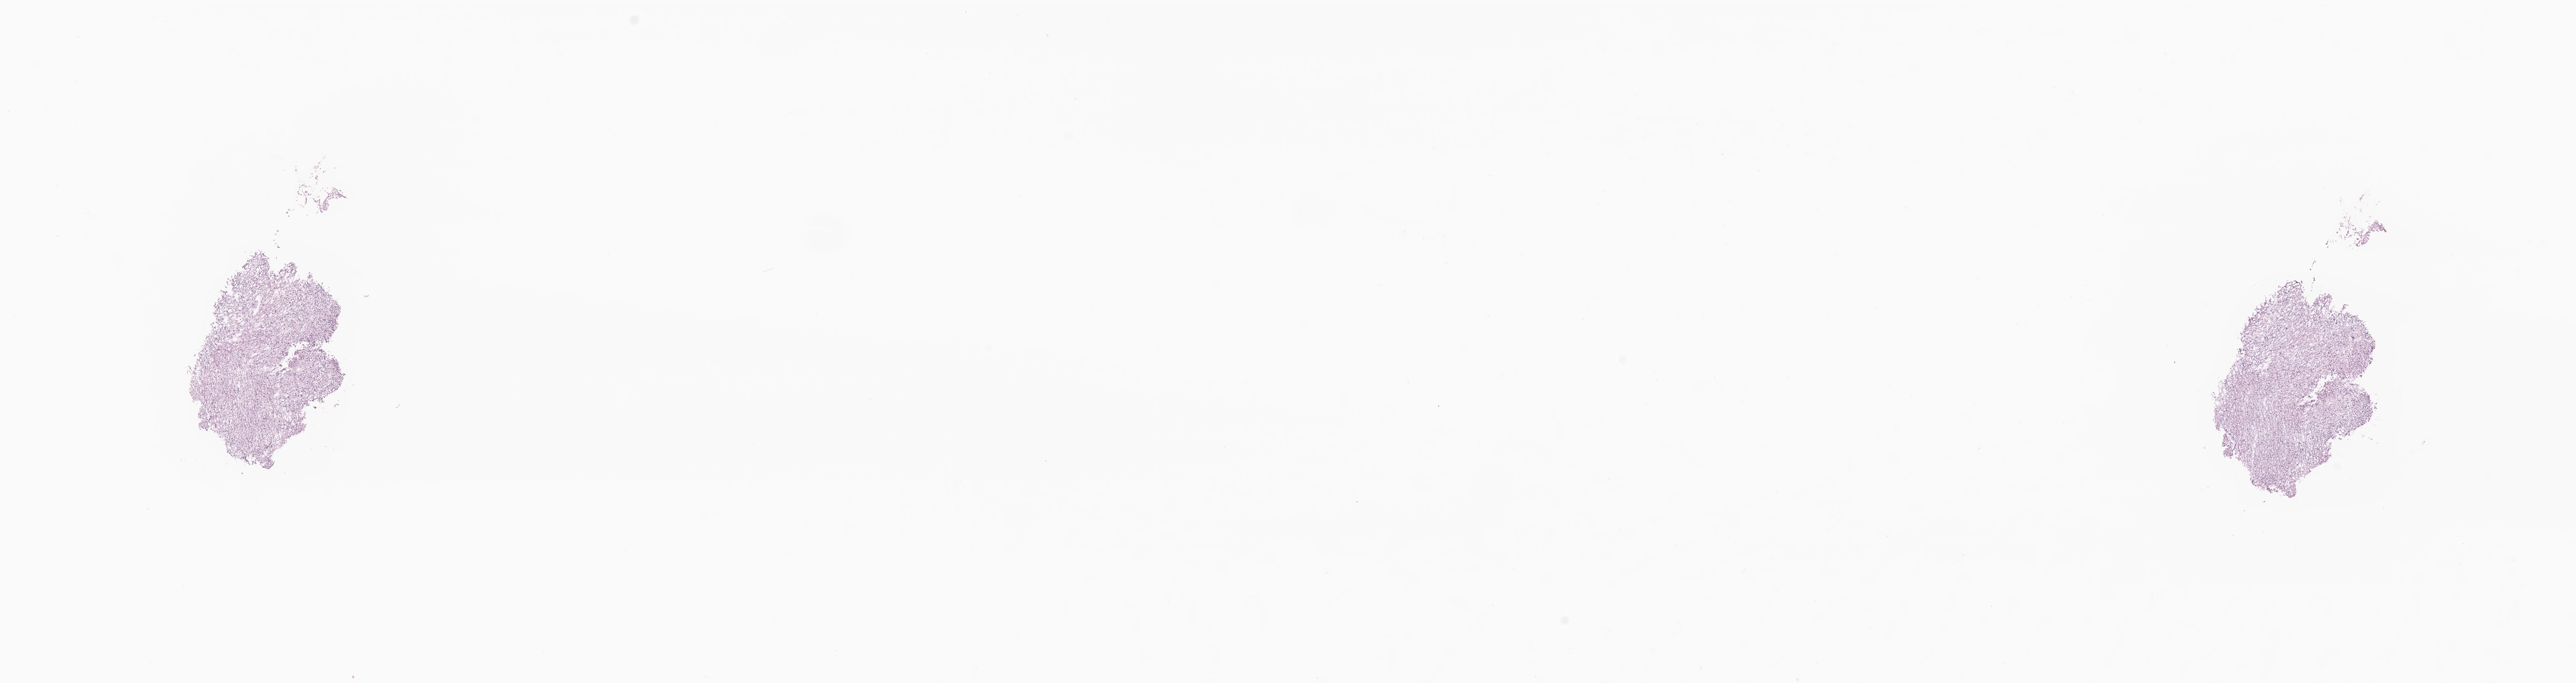
Whole-slide image, haematoxylin and eosin stain of tumor tissue from the brain — low-resolution overview of the scanned area, about 26.6 x 7.0 mm. Frozen section (OCT-embedded). Male patient, age 65 months.
Diagnosis: Glioma, malignant.